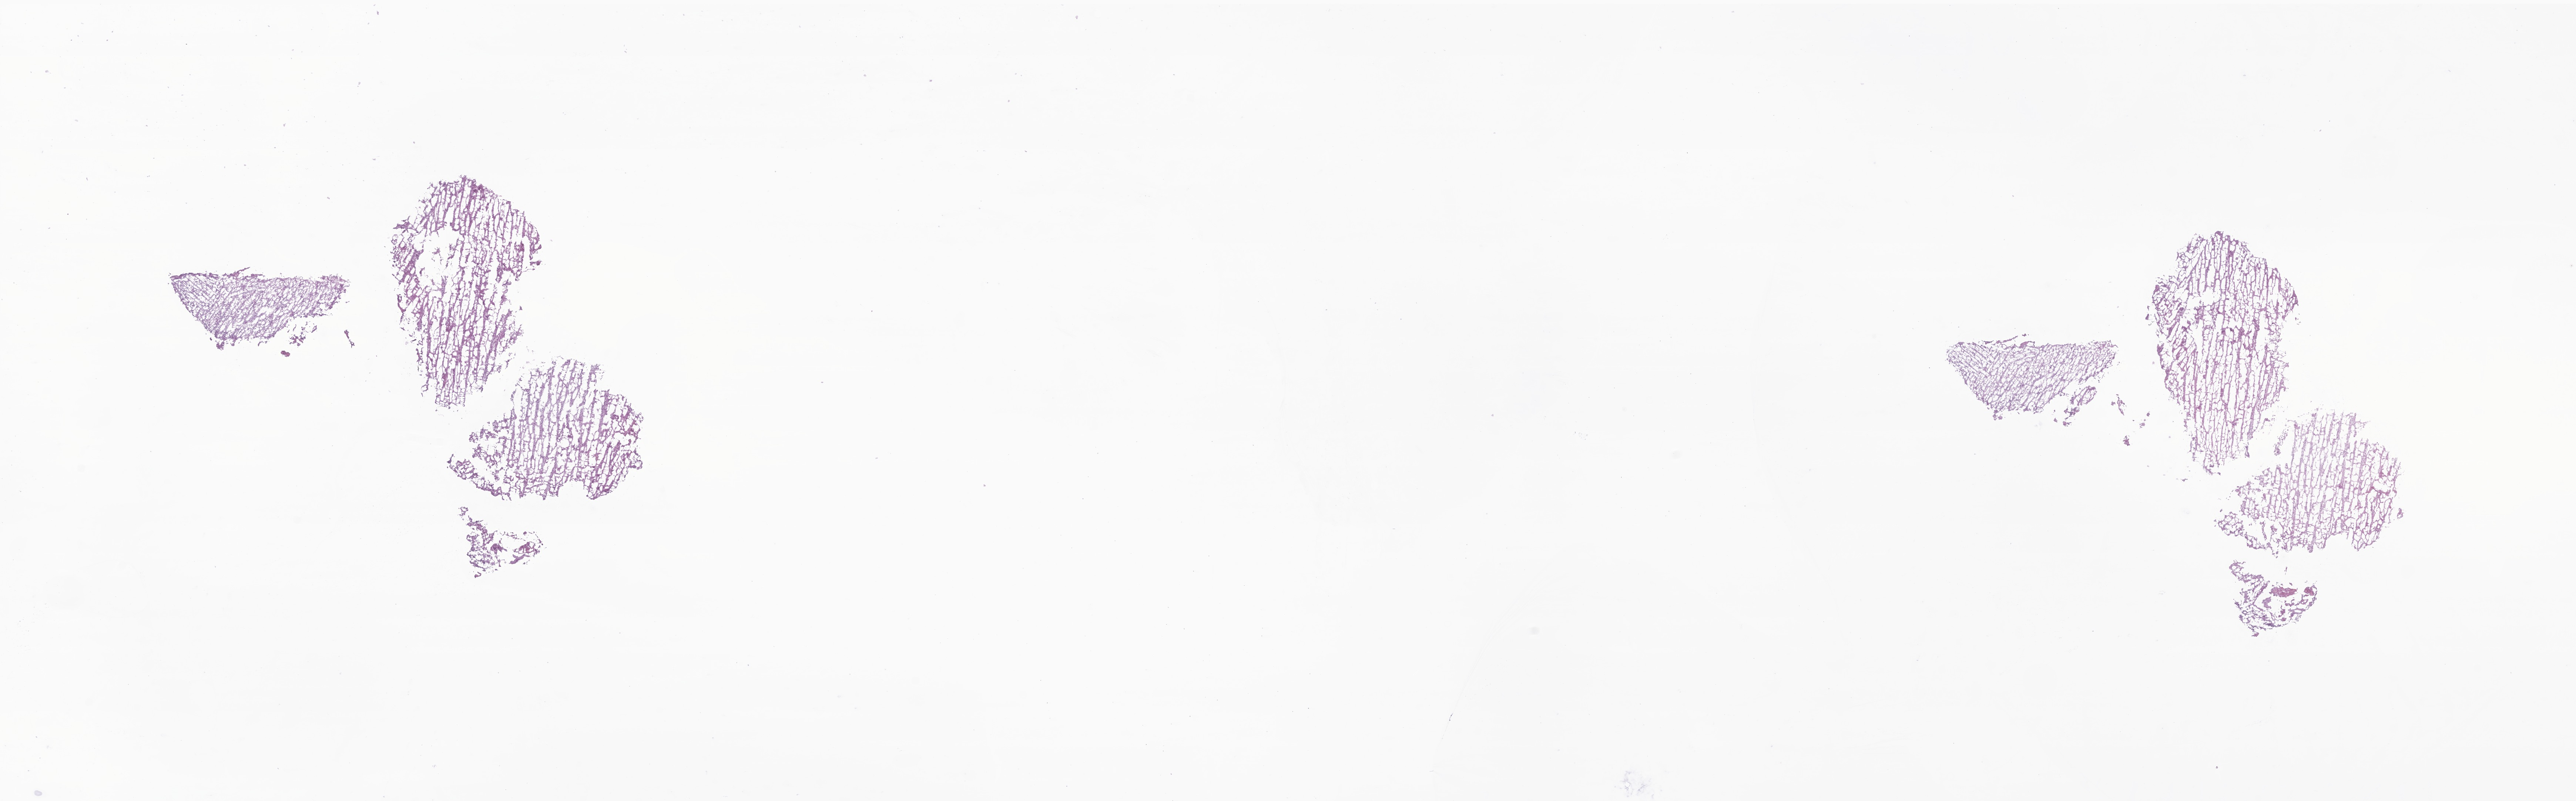
Whole-slide image, haematoxylin and eosin stain of tumor tissue from the cerebellum — shown as a low-resolution overview of the whole scanned area (about 29.3 x 9.1 mm). Frozen section. Patient: male, age 619 days (about 1.7 years).
Diagnosis (ICD-O-3 morphology term): Ependymoma, NOS.